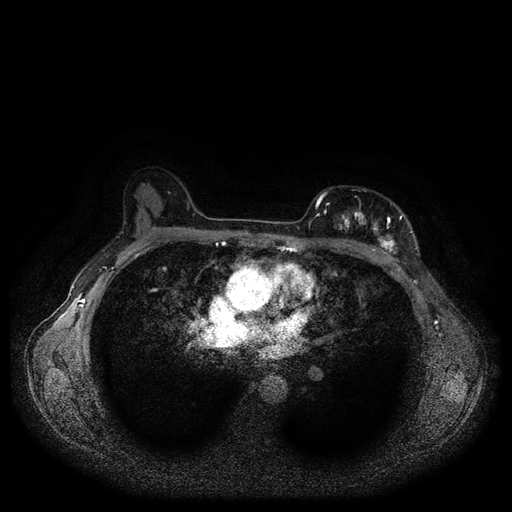
Breast MRI (dynamic contrast-enhanced, multi-phase), one axial slice. Slice 66 of 116 in the series (ordered by position). Dynamic contrast-enhanced series, time point 2 of 5 at this slice position (early post-contrast). 1.5 T. TE 2.6 ms, TR 5.3 ms. 2 mm slice thickness. 512 × 512 image matrix, field of view 350 × 350 mm. Female patient, age 51 years.
Structures marked on this image (semi-automatic segmentation, software-assisted and operator-edited):
- breast lesion (labelled 'tumour' in the annotation; benign lesions carry a separate 'benign' label): bounding box <332,204,398,257> (left, top, right, bottom; pixels)